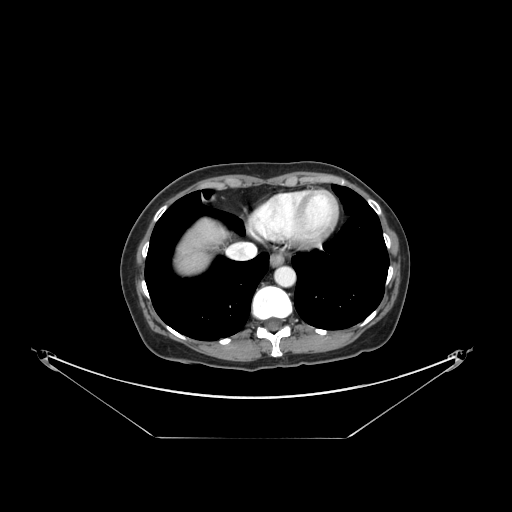
Contrast-enhanced abdominal CT, one axial slice. Position 136 of 148 along the scan axis. 120 kVp. Intravenous contrast given. Soft-tissue window (W 400 / L 40 HU). 512 × 512 image matrix, field of view 500 × 500 mm. Female patient, age 73 years. From the clinical record (not read from this slice): diagnosis: colorectal cancer liver metastases, imaged before liver resection; multiple liver metastases: no; largest metastasis: 1 cm; chemotherapy before resection: yes.
Annotated regions visible in this slice (outlined manually by an expert reader):
- liver: box from (x=178, y=221) to (x=223, y=275) px
- planned liver remnant (the part of the liver to remain after resection): (x=223, y=228)–(x=227, y=234)